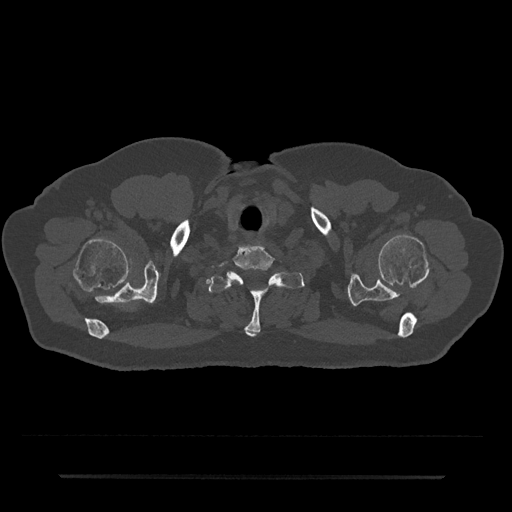
CT including the spine, one axial slice; slice 654 of 797 in the series (ordered by position); 120 kVp; bone window (W 1800 / L 400 HU); 0.5 mm slice thickness; 512 × 512 image matrix, field of view 437 × 437 mm. Patient: male, 69 years. Case-level facts recorded for this patient, not image findings: primary cancer: prostate.
Structures marked on this image (semi-automatic segmentation, software-assisted and operator-edited):
- T1 vertebra: bounding box <208,272,304,337> (left, top, right, bottom; pixels)